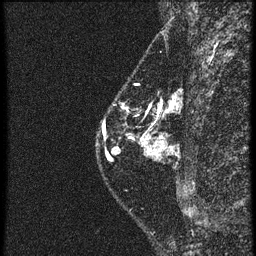
Breast MRI (dynamic contrast-enhanced), one sagittal slice. Position 18 of 60 along the scan axis. 4 images stored at this slice position (order not interpretable as contrast timing). 1.5 T. TE 4.2 ms, TR 20.4 ms. 1.5 mm slice thickness. 256 × 256 image matrix. Female patient, age 46 years. From the clinical record (not read from this slice): setting: breast cancer imaged before/during neoadjuvant chemotherapy; receptor status: triple-negative.
Structures marked on this image (semi-automatic segmentation, software-assisted and operator-edited):
- analysis volume of interest (the breast-tissue region the enhancement analysis was run in; not a lesion): bounding box <96,82,163,185> (left, top, right, bottom; pixels)
- tumour enhancement mask (voxels above the 90 % enhancement threshold inside the analysis volume of interest): <104,126,119,155>